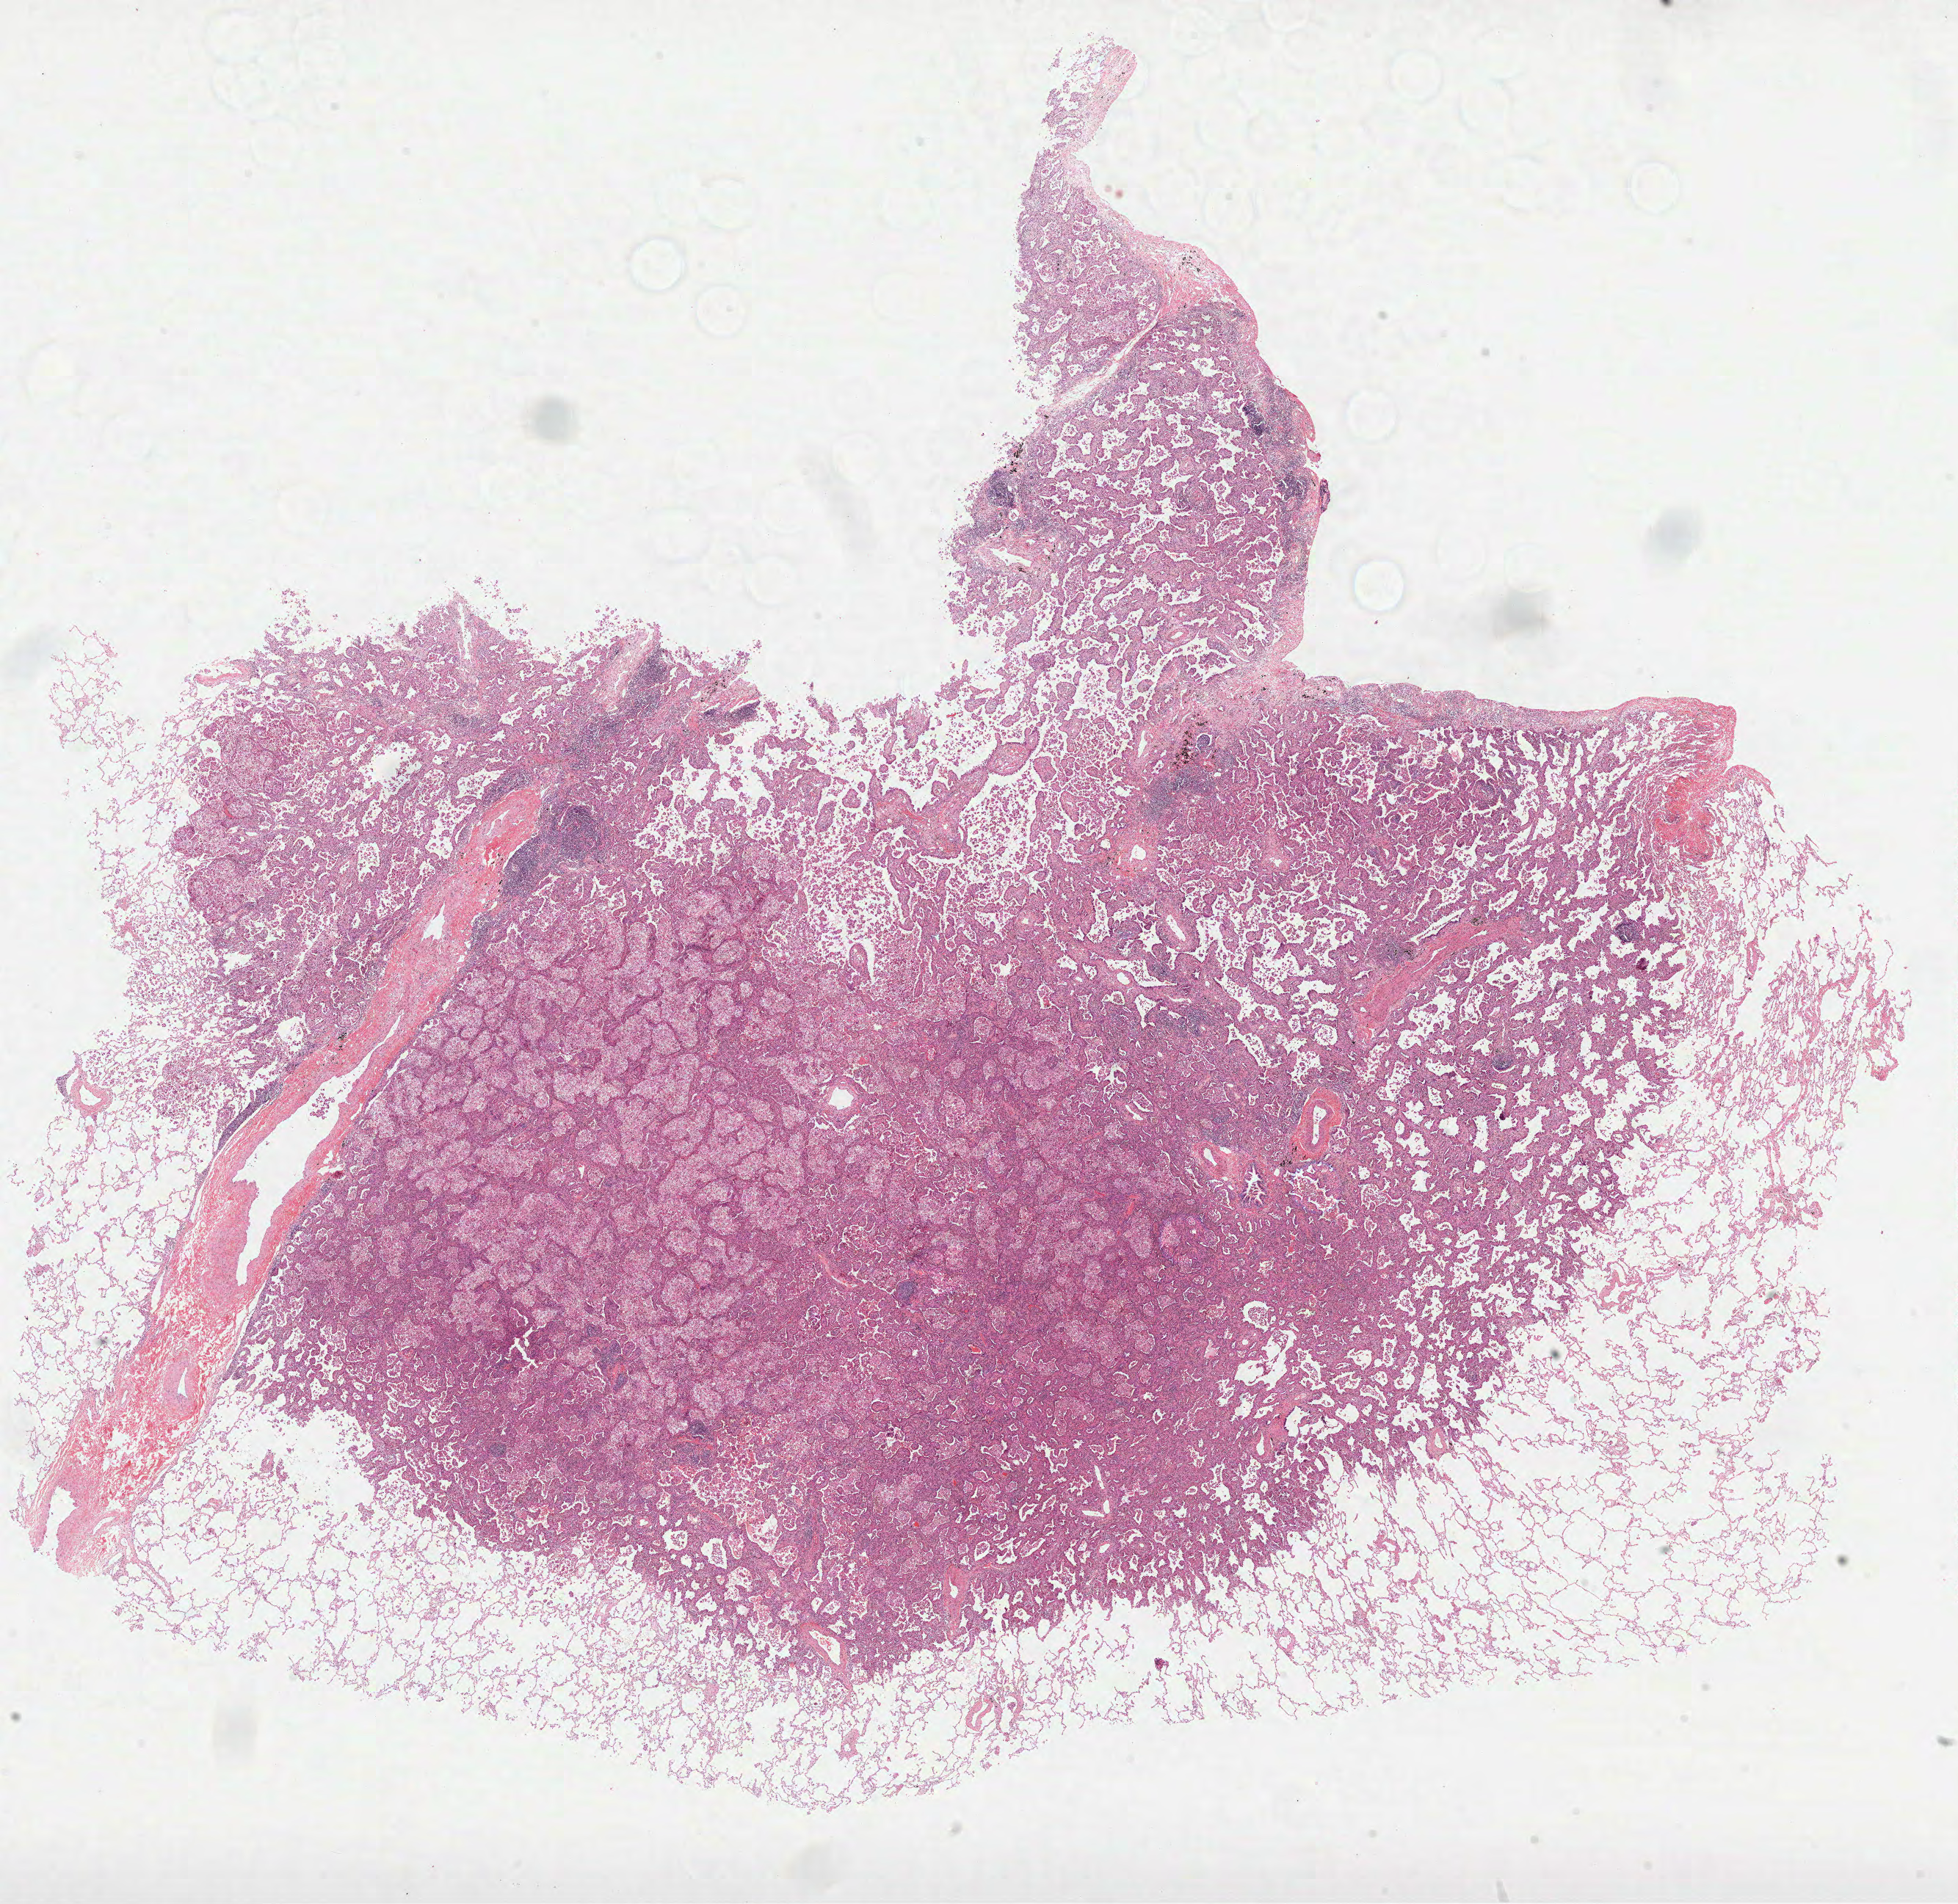
H&E-stained whole-slide image — a low-resolution overview of the entire scanned area, about 21.5 x 20.9 mm (slide scanned at 40x); formalin-fixed paraffin-embedded (FFPE) diagnostic section; sample: primary tumour, lung. Female, age 61 years at initial diagnosis.
AJCC pathologic stage: IA (7th edition). TNM: T1b N0 M0. Pathologic diagnosis: Bronchio-alveolar carcinoma, mucinous (lower lobe, lung).